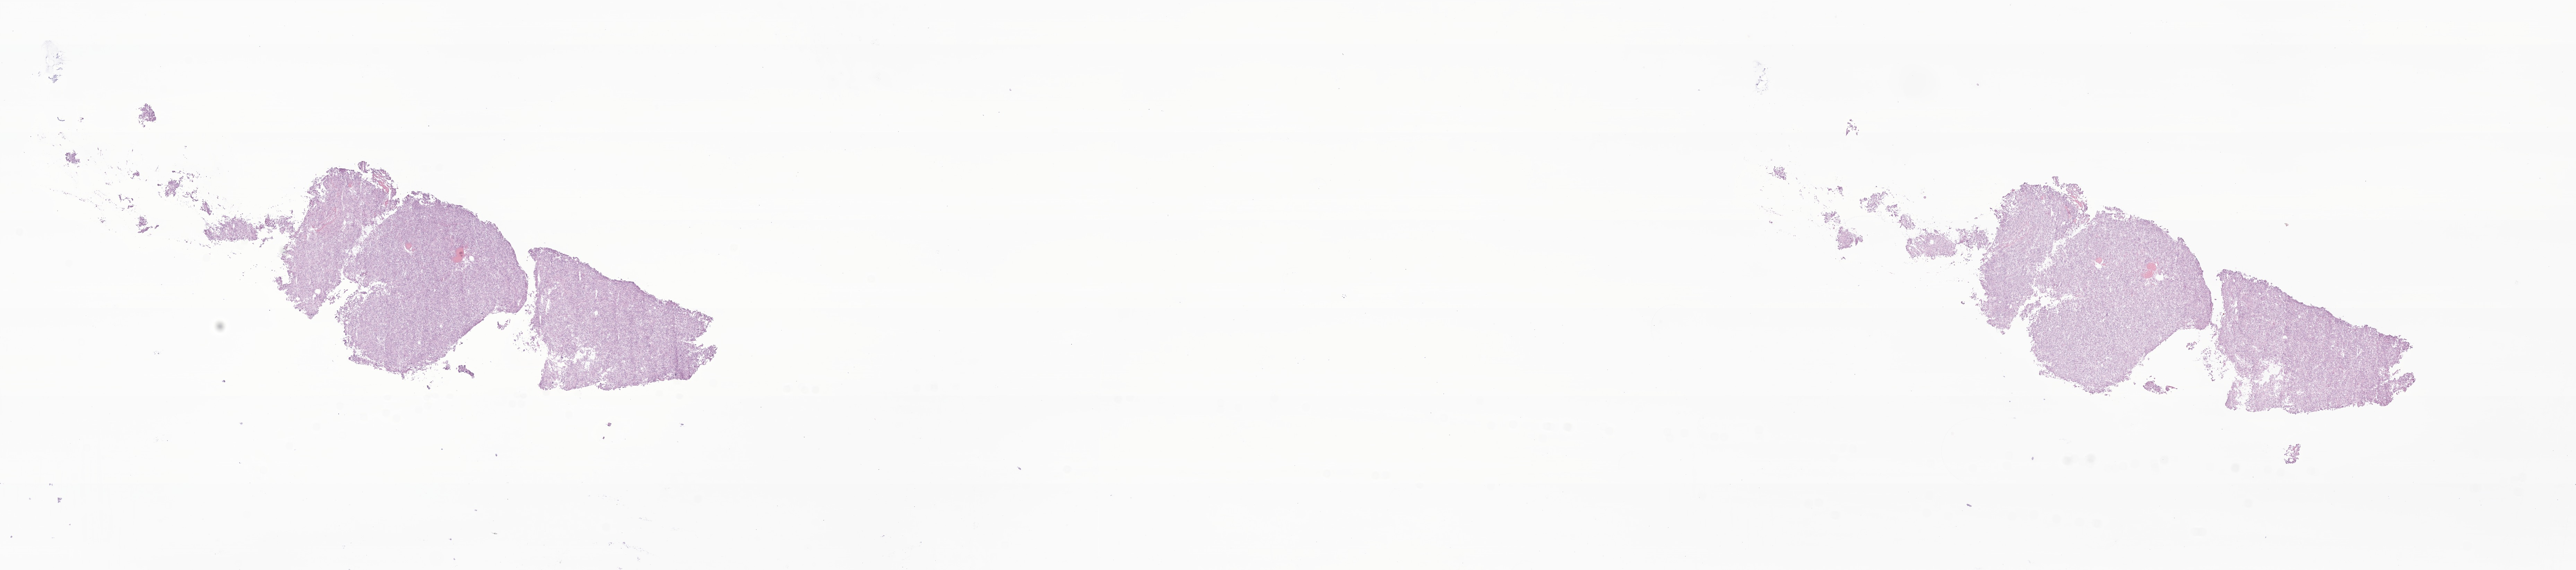
Whole-slide image, H&E stain of tumor tissue from the brain, low-resolution overview of the scanned area, about 31.3 x 6.9 mm, frozen section (OCT-embedded). Patient: female, age 165 months (13 years 9 months).
Recorded diagnosis: Atypical meningioma.